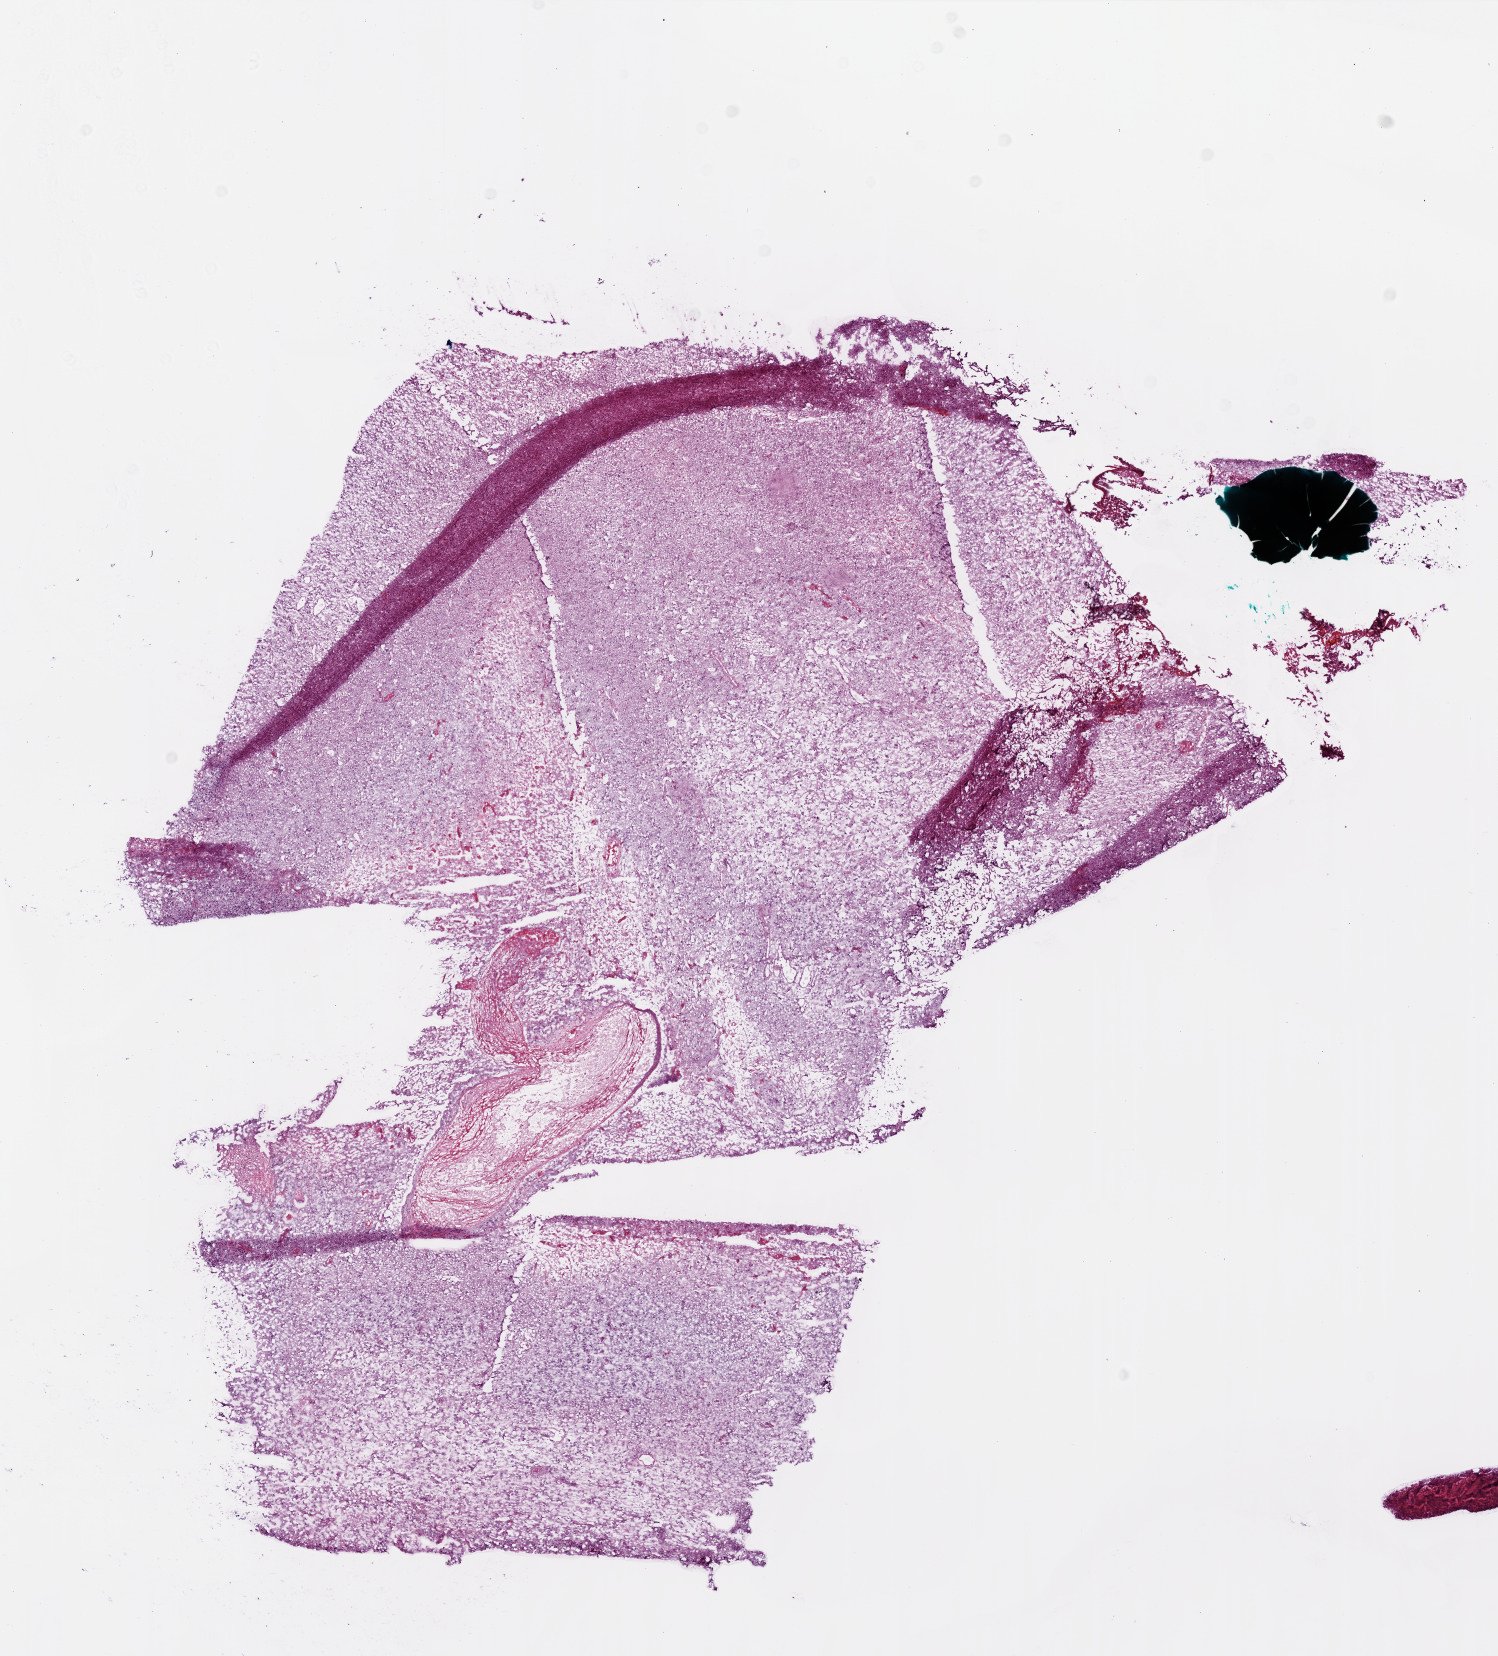
Digitized Hematoxylin and eosin (H&E) stained tissue section (whole slide) — shown as a low-resolution overview of the whole scanned area (about 12.0 x 13.3 mm, acquisition: 20x scan), frozen section, brain, primary tumour sample. Male patient; age at initial diagnosis 71 years. Slide review estimates, as recorded: tumour cells 95%, tumour nuclei 90%, normal cells 0%, stromal cells 0%, necrosis 5%.
Diagnosis: Glioblastoma.